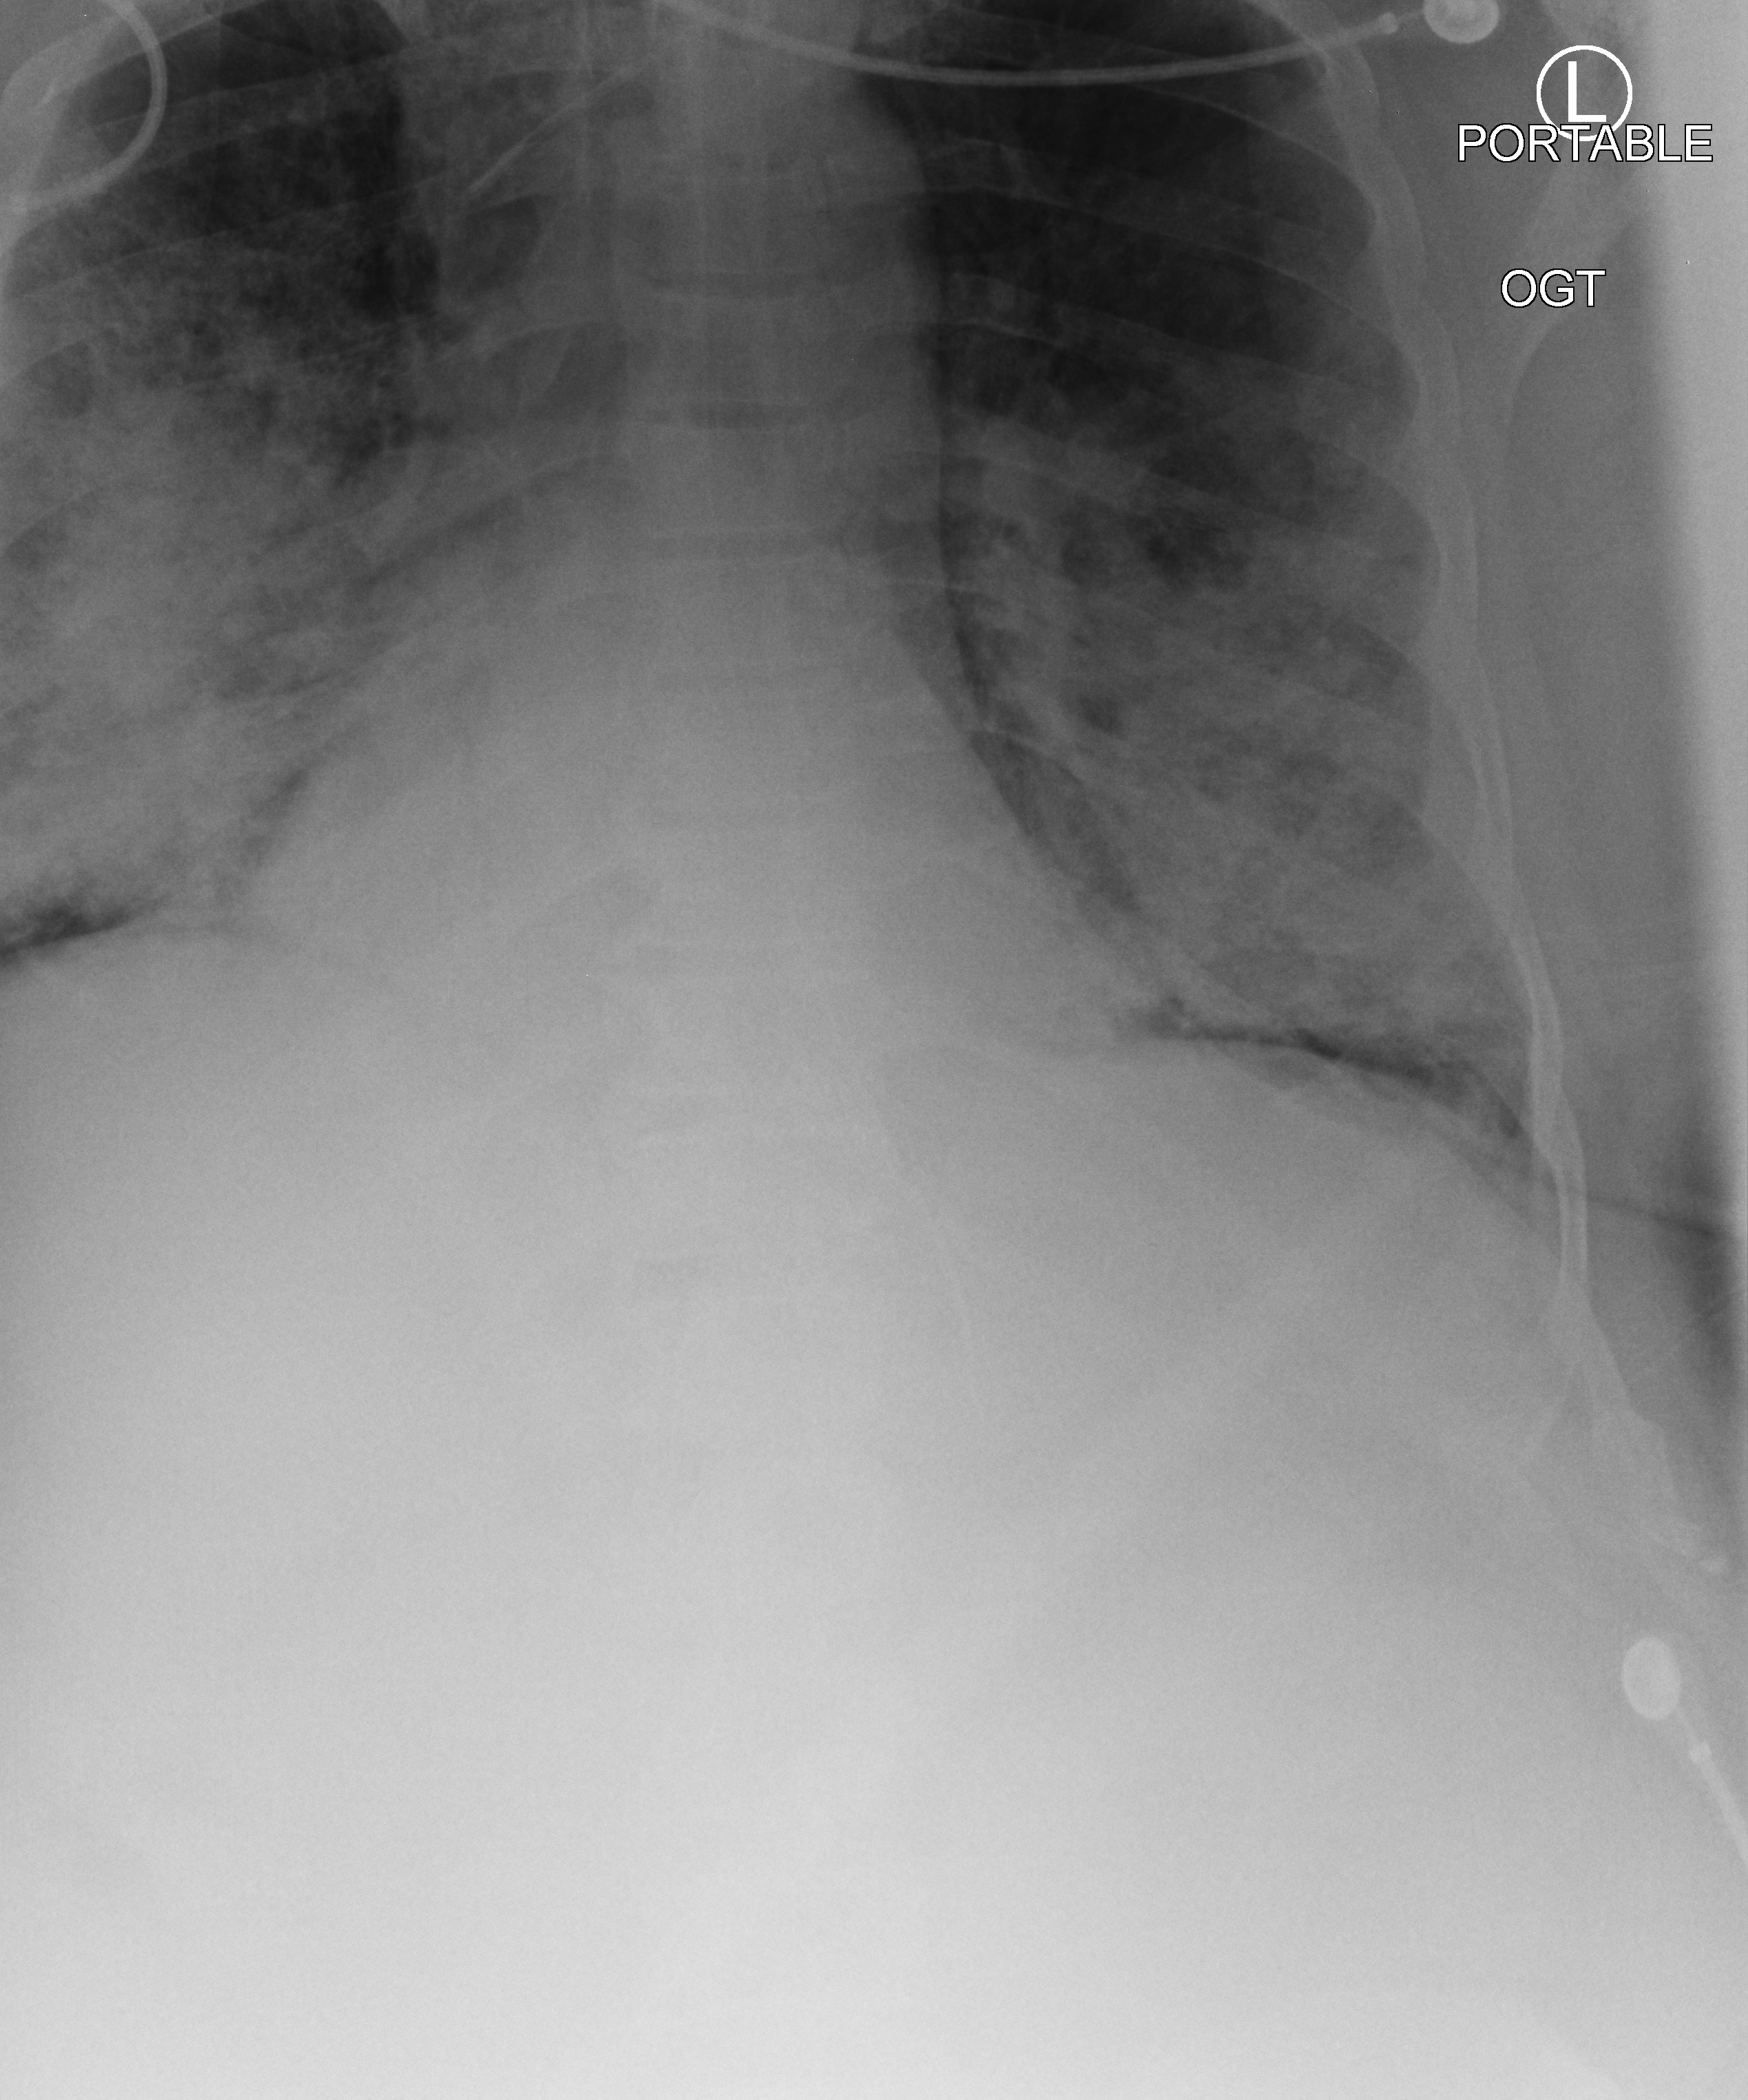
Portable chest radiograph. Adult patient hospitalised with COVID-19, age 18–59 years.
Hospital-stay facts (about this admission, not read from this image; timing relative to this image not recorded): length of hospital stay: 13 days.